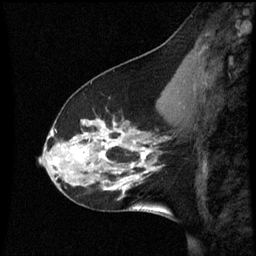
Breast MRI (dynamic contrast-enhanced), one sagittal slice. Slice 21 of 60 in the series (ordered by position). Dynamic contrast-enhanced series, image 2 of 3 at this slice position (ordered by acquisition). 1.5 T. TE 4.2 ms, TR 8.9 ms. 256 × 256 image matrix, field of view 200 × 200 mm. Patient: female, 45 years. From the clinical record (not read from this slice): setting: breast cancer imaged before/during neoadjuvant chemotherapy; receptor status: HR-positive, HER2-negative.
Structures marked on this image (semi-automatic segmentation, software-assisted and operator-edited):
- analysis volume of interest (the breast-tissue region the enhancement analysis was run in; not a lesion): bounding box (x1, y1, x2, y2) in pixels: (46, 94, 171, 205)
- tumour enhancement mask (voxels above the 70 % enhancement threshold inside the analysis volume of interest): (52, 124, 151, 185)